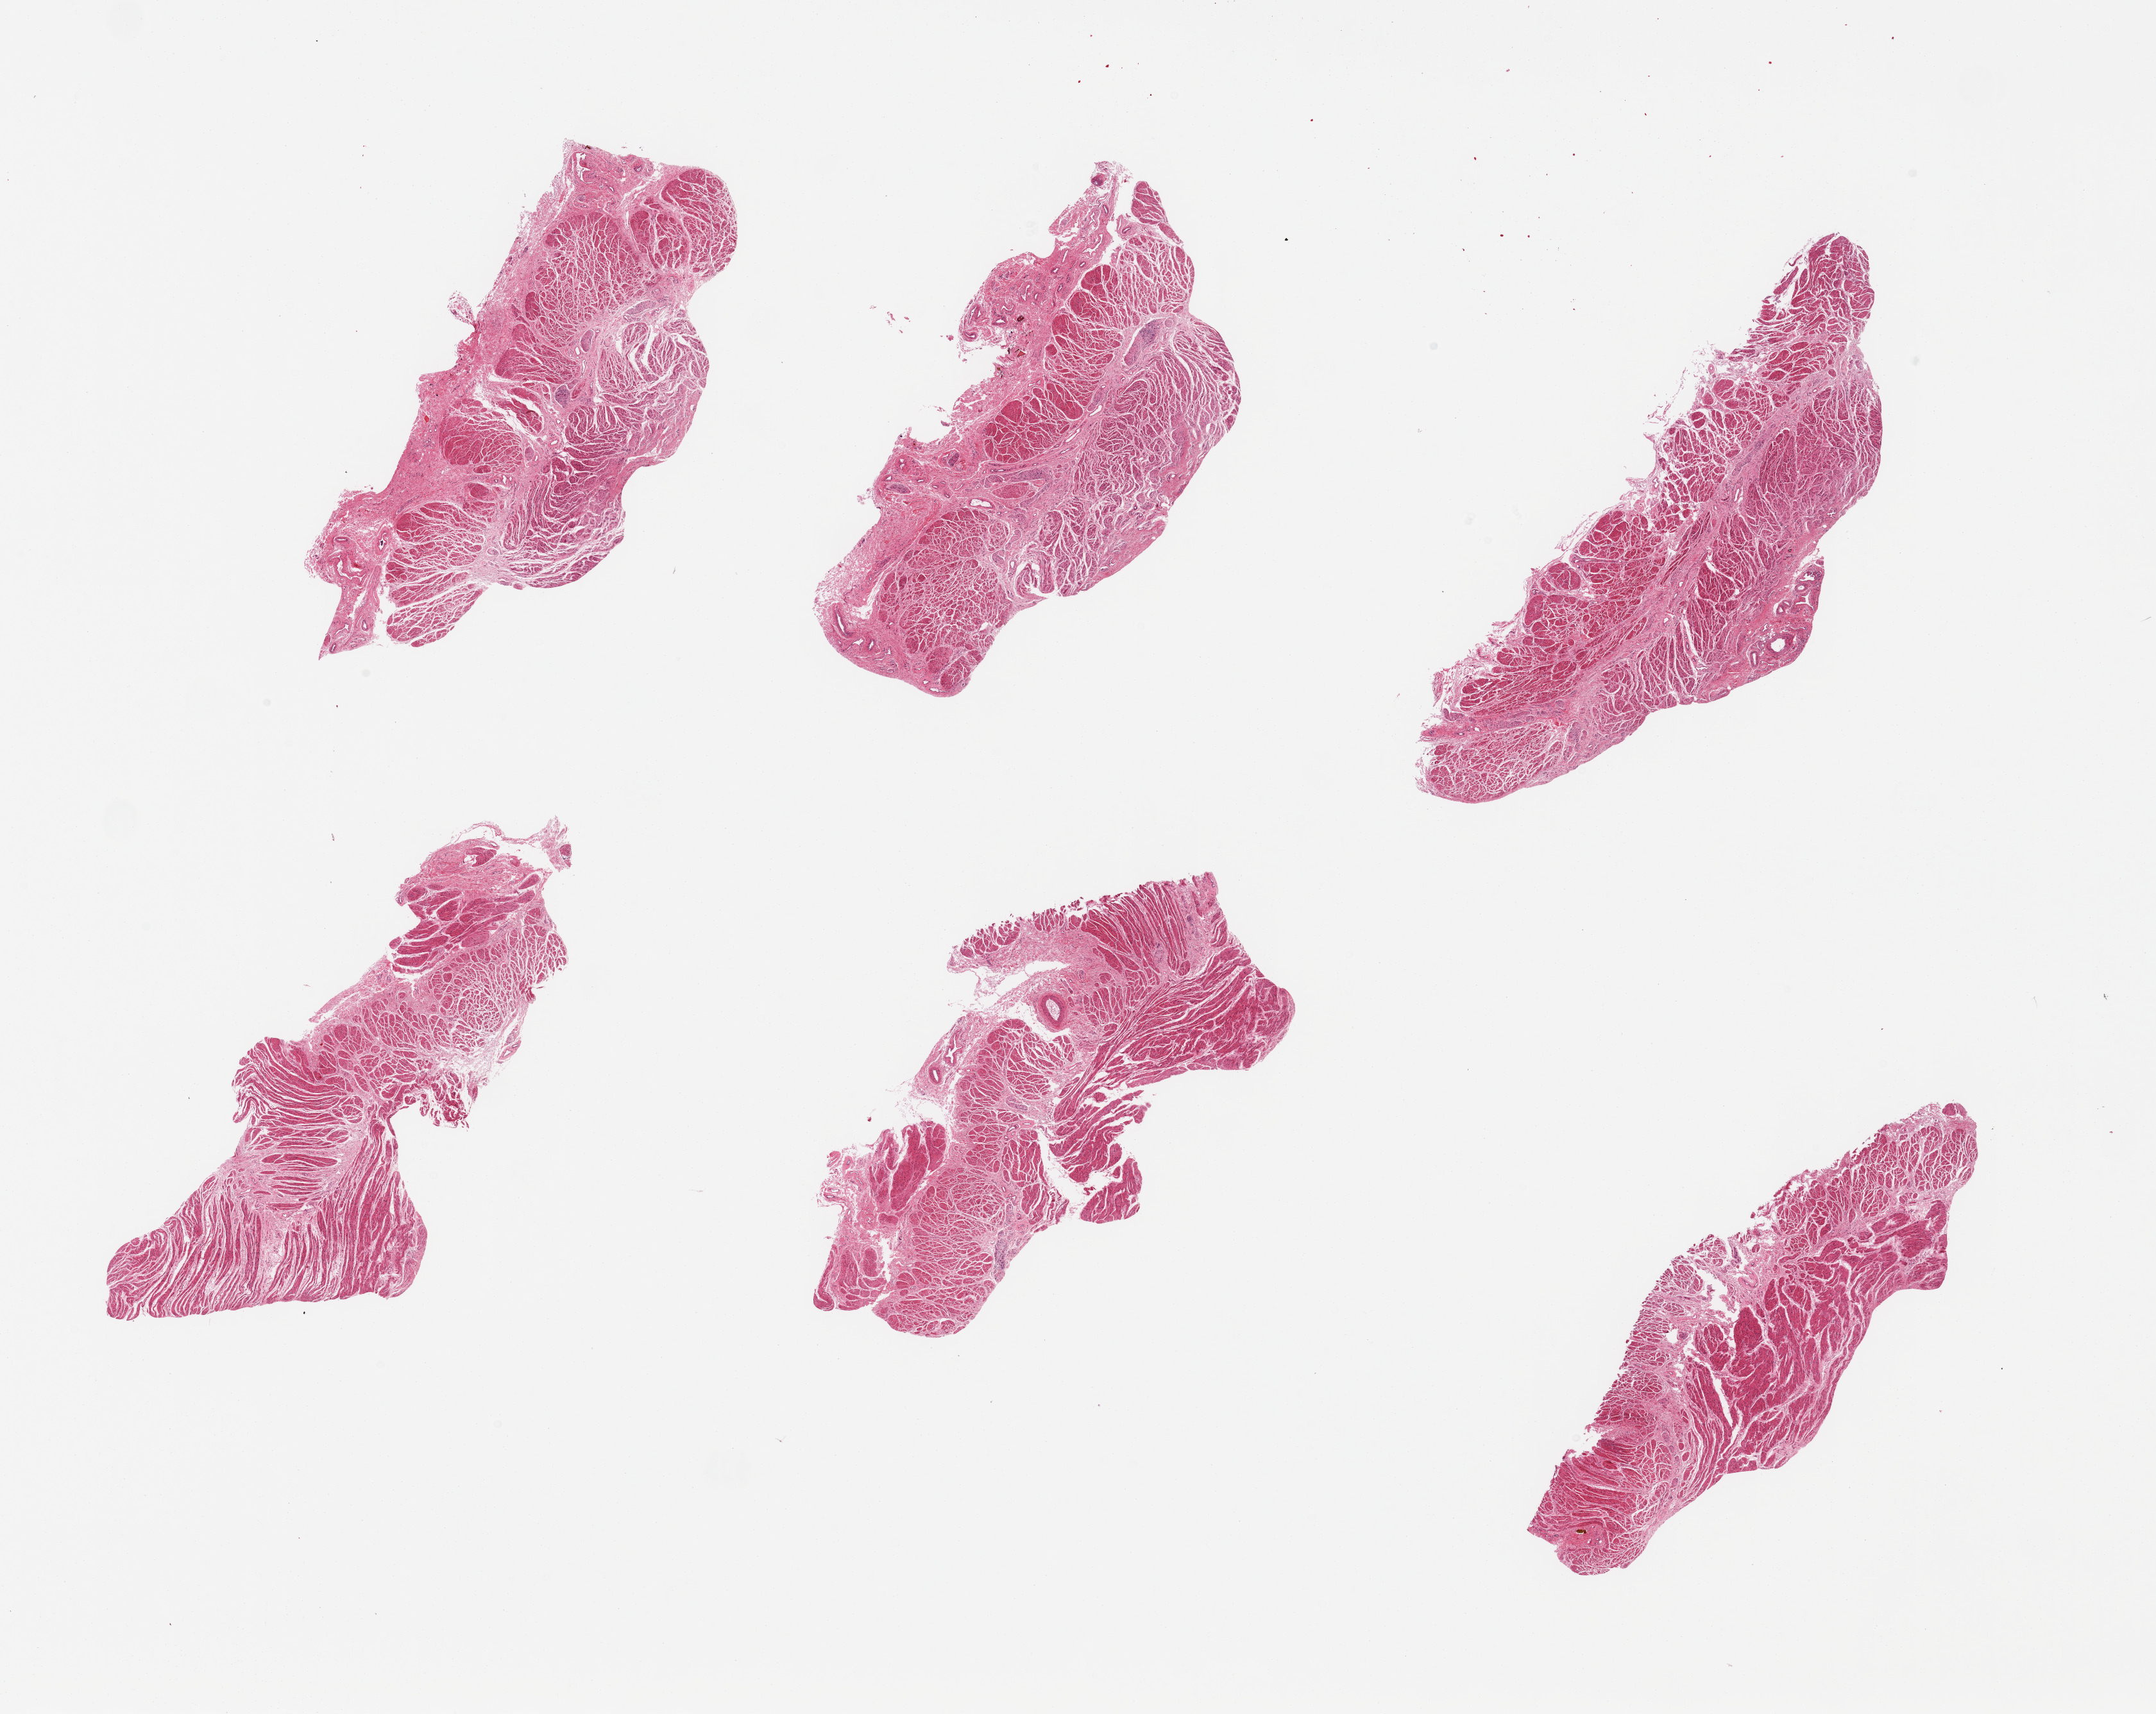
Whole-slide image, haematoxylin and eosin stain, shown as a low-resolution overview of the whole scanned area (about 26.6 x 21.1 mm); PAXgene-fixed paraffin-embedded (PFPE) section; section of gastroesophageal junction (target tissue); donor tissue sample. Donor: male.
Reviewer comment on this tissue sample: 6 pieces; all have 10% interstitial fibrous content.